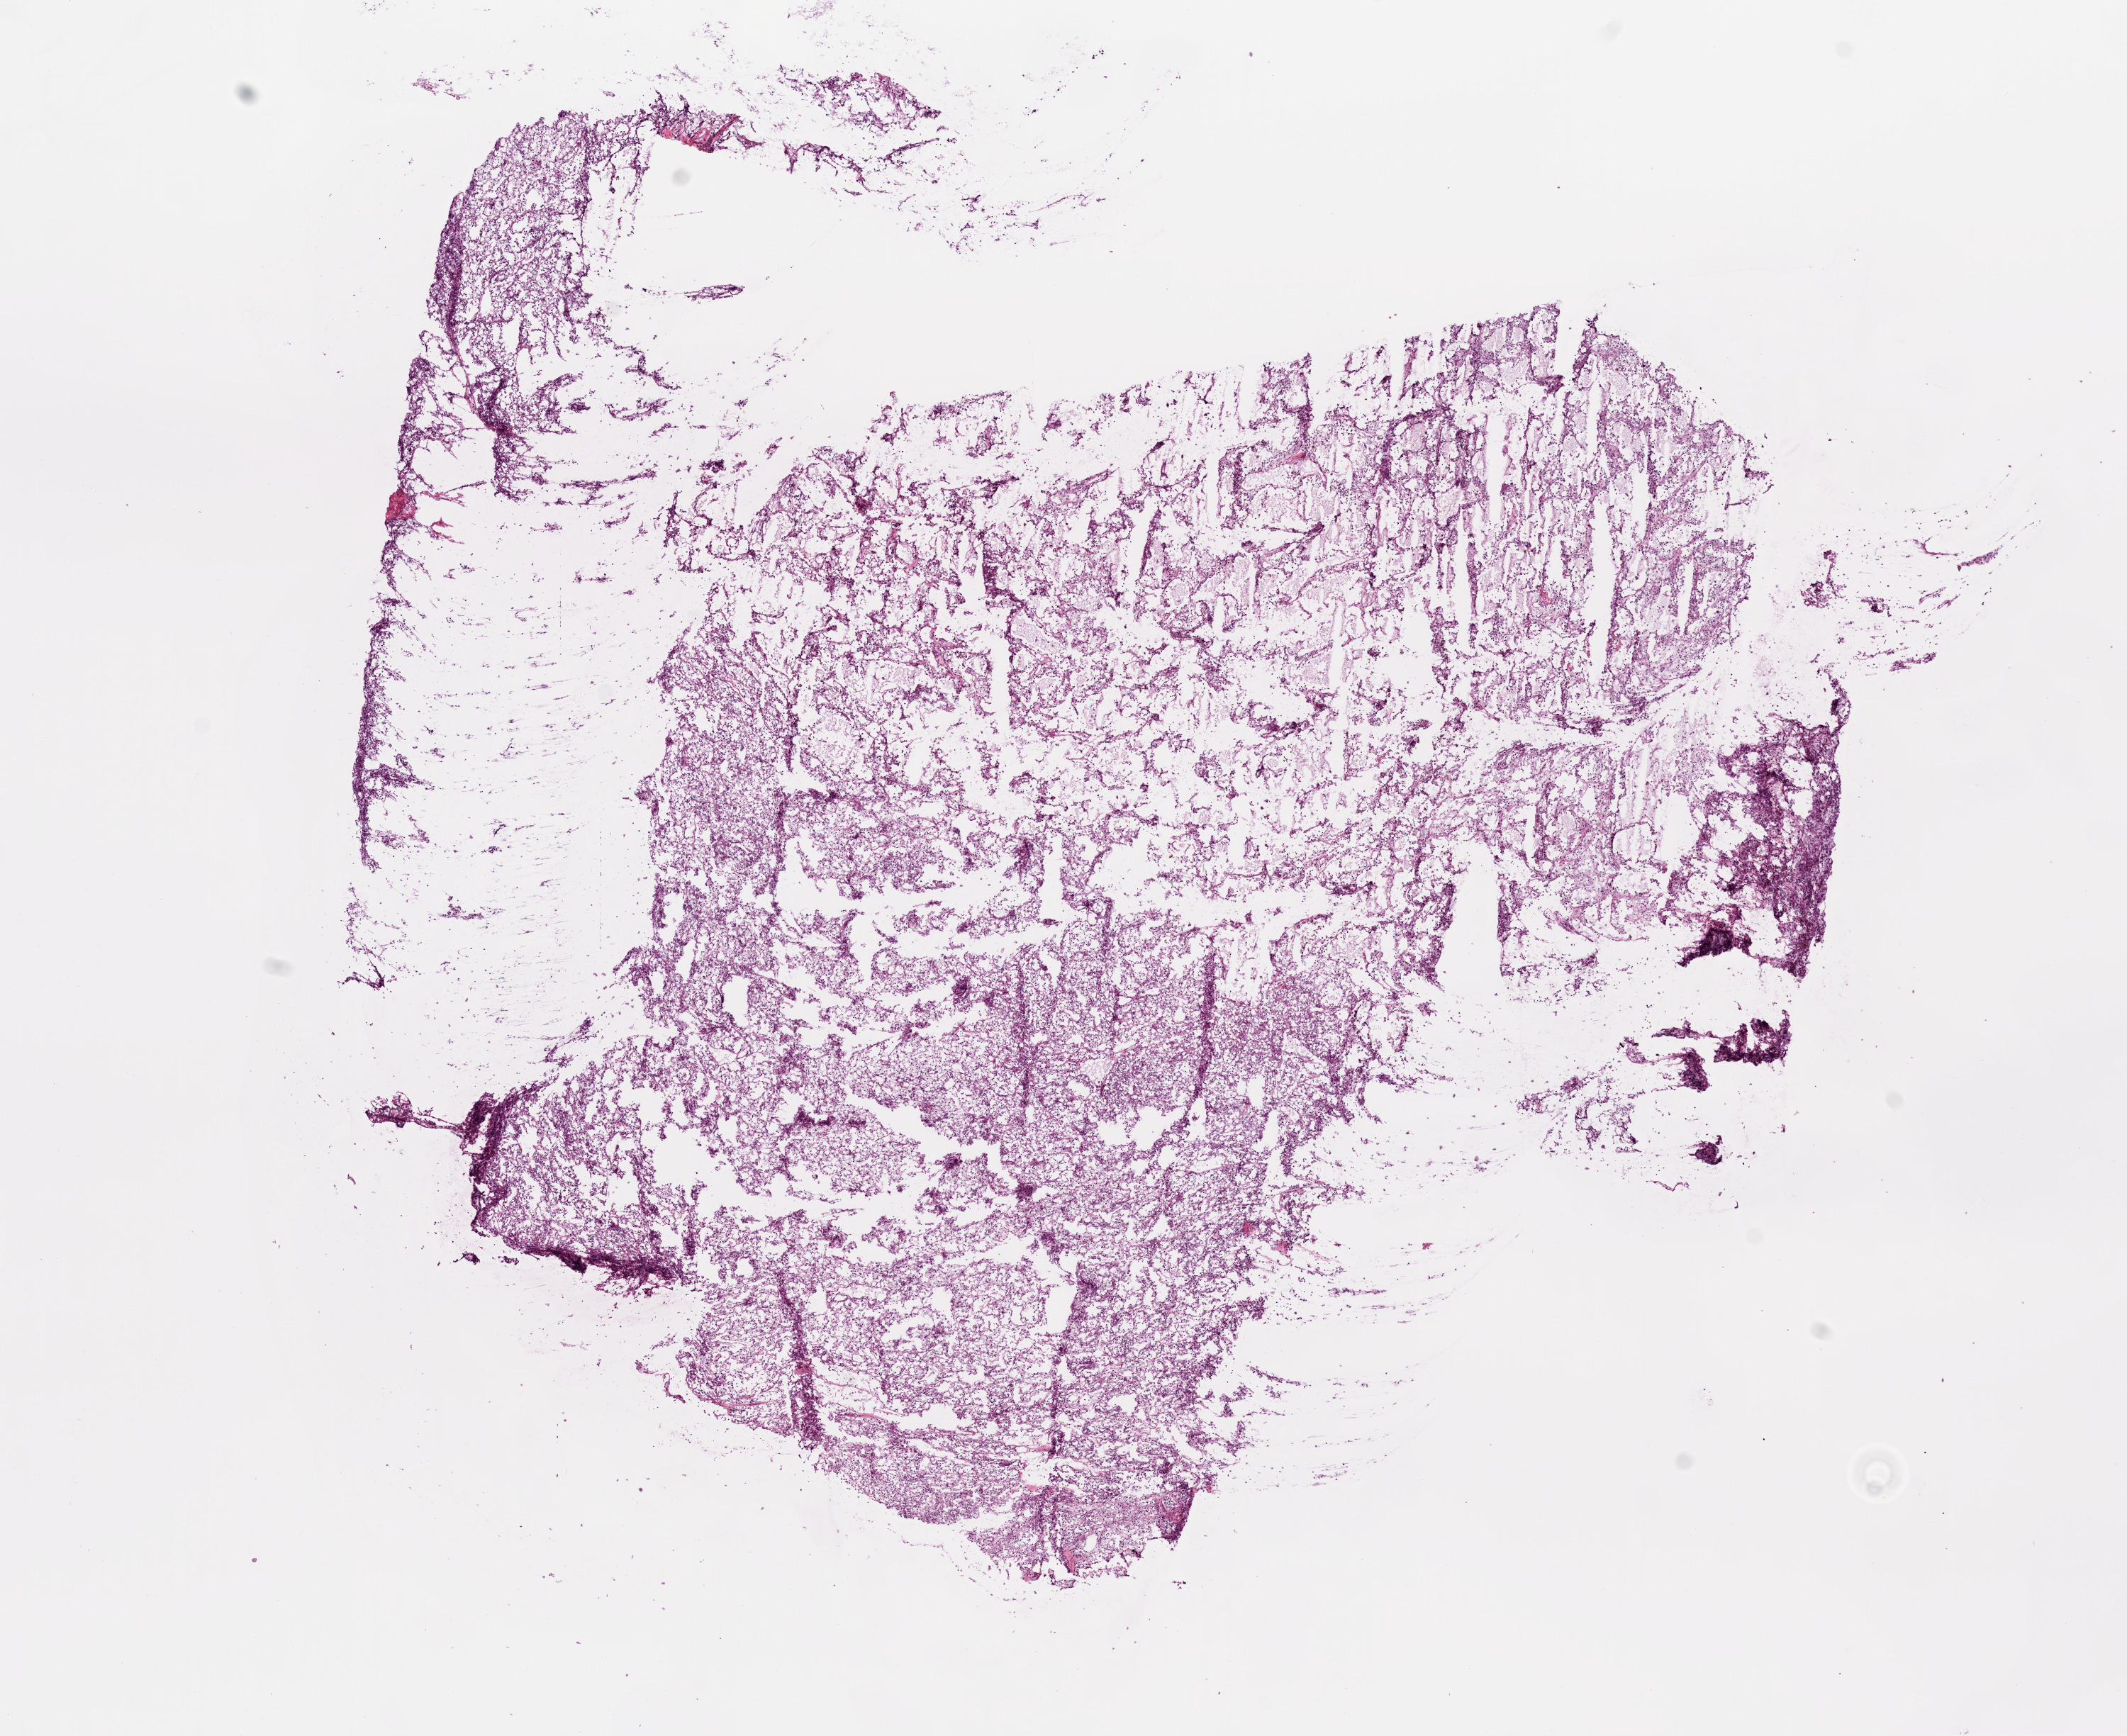
Digitized Hematoxylin and eosin (H&E) stained tissue section (whole slide), shown as a low-resolution overview of the whole scanned area (about 12.0 x 9.8 mm, slide scanned at 20x). Frozen section from the top of the tissue portion. Kidney, primary tumour sample. Female patient; age at initial diagnosis 66 years. Histologic grade: G3 (poorly differentiated). Pathologist review of this section (percent, as recorded): tumour cells 95%, tumour nuclei 85%, normal cells 0%, stromal cells 5%, necrosis 0%.
- AJCC pathologic stage: III
- laterality: right
- pathologic diagnosis: Clear cell adenocarcinoma, NOS